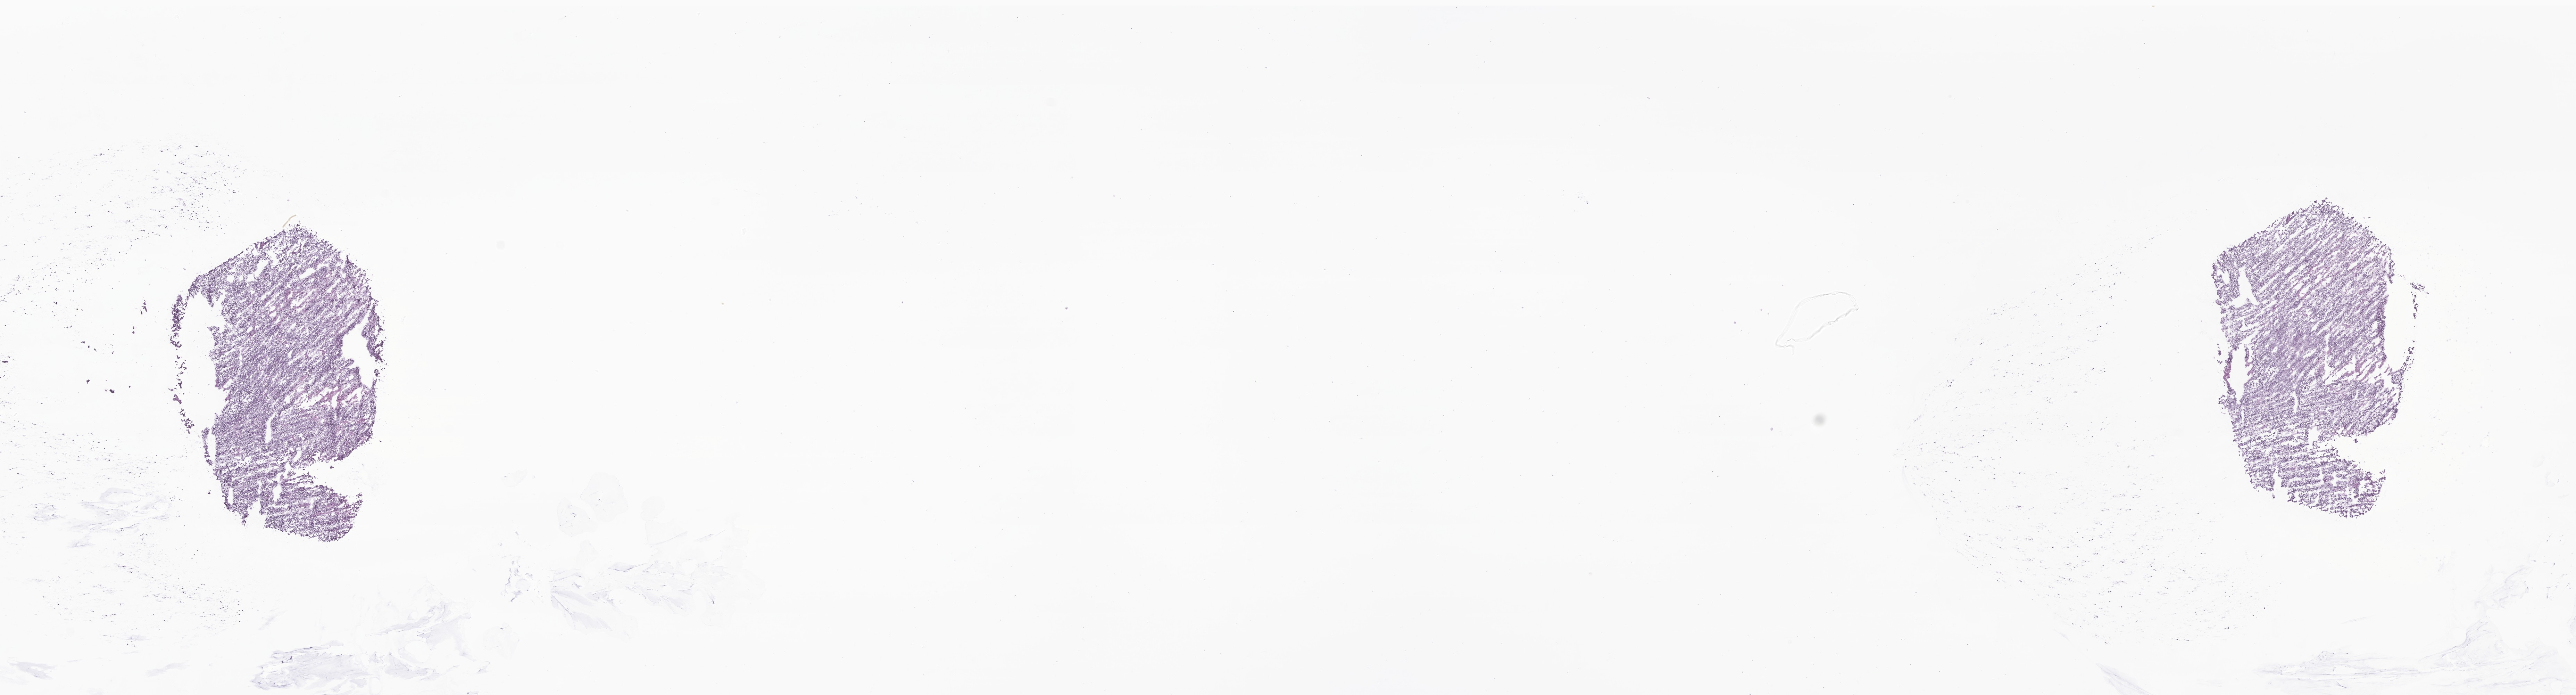
Haematoxylin and eosin whole-slide image of tumor tissue from the cerebellum, a low-resolution overview of the entire scanned area, about 31.3 x 8.4 mm, frozen section (OCT-embedded). Patient male; age 109 months (9 years 1 month).
Recorded diagnosis: Medulloblastoma, NOS.